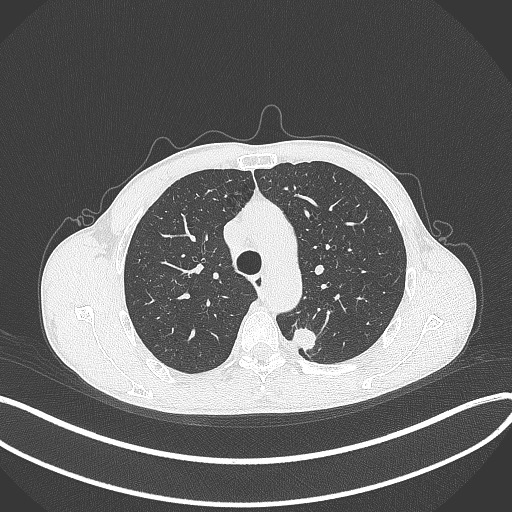
Chest CT, one axial slice. Slice 288 of 429 in the series (ordered by position). Reconstruction kernel B70f. 120 kVp. Lung window (W 1500 / L -600 HU). 1 mm slice thickness. 512 × 512 image matrix, field of view 400 × 400 mm. Patient: male, 51 years. From the clinical record (not read from this slice): clinical TNM (as recorded): T2a N1 M1.
Outlined on this slice (bounding box drawn by a radiologist):
- lung tumour (recorded histology: adenocarcinoma): bounding box (x1, y1, x2, y2) in pixels: (290, 325, 319, 353)